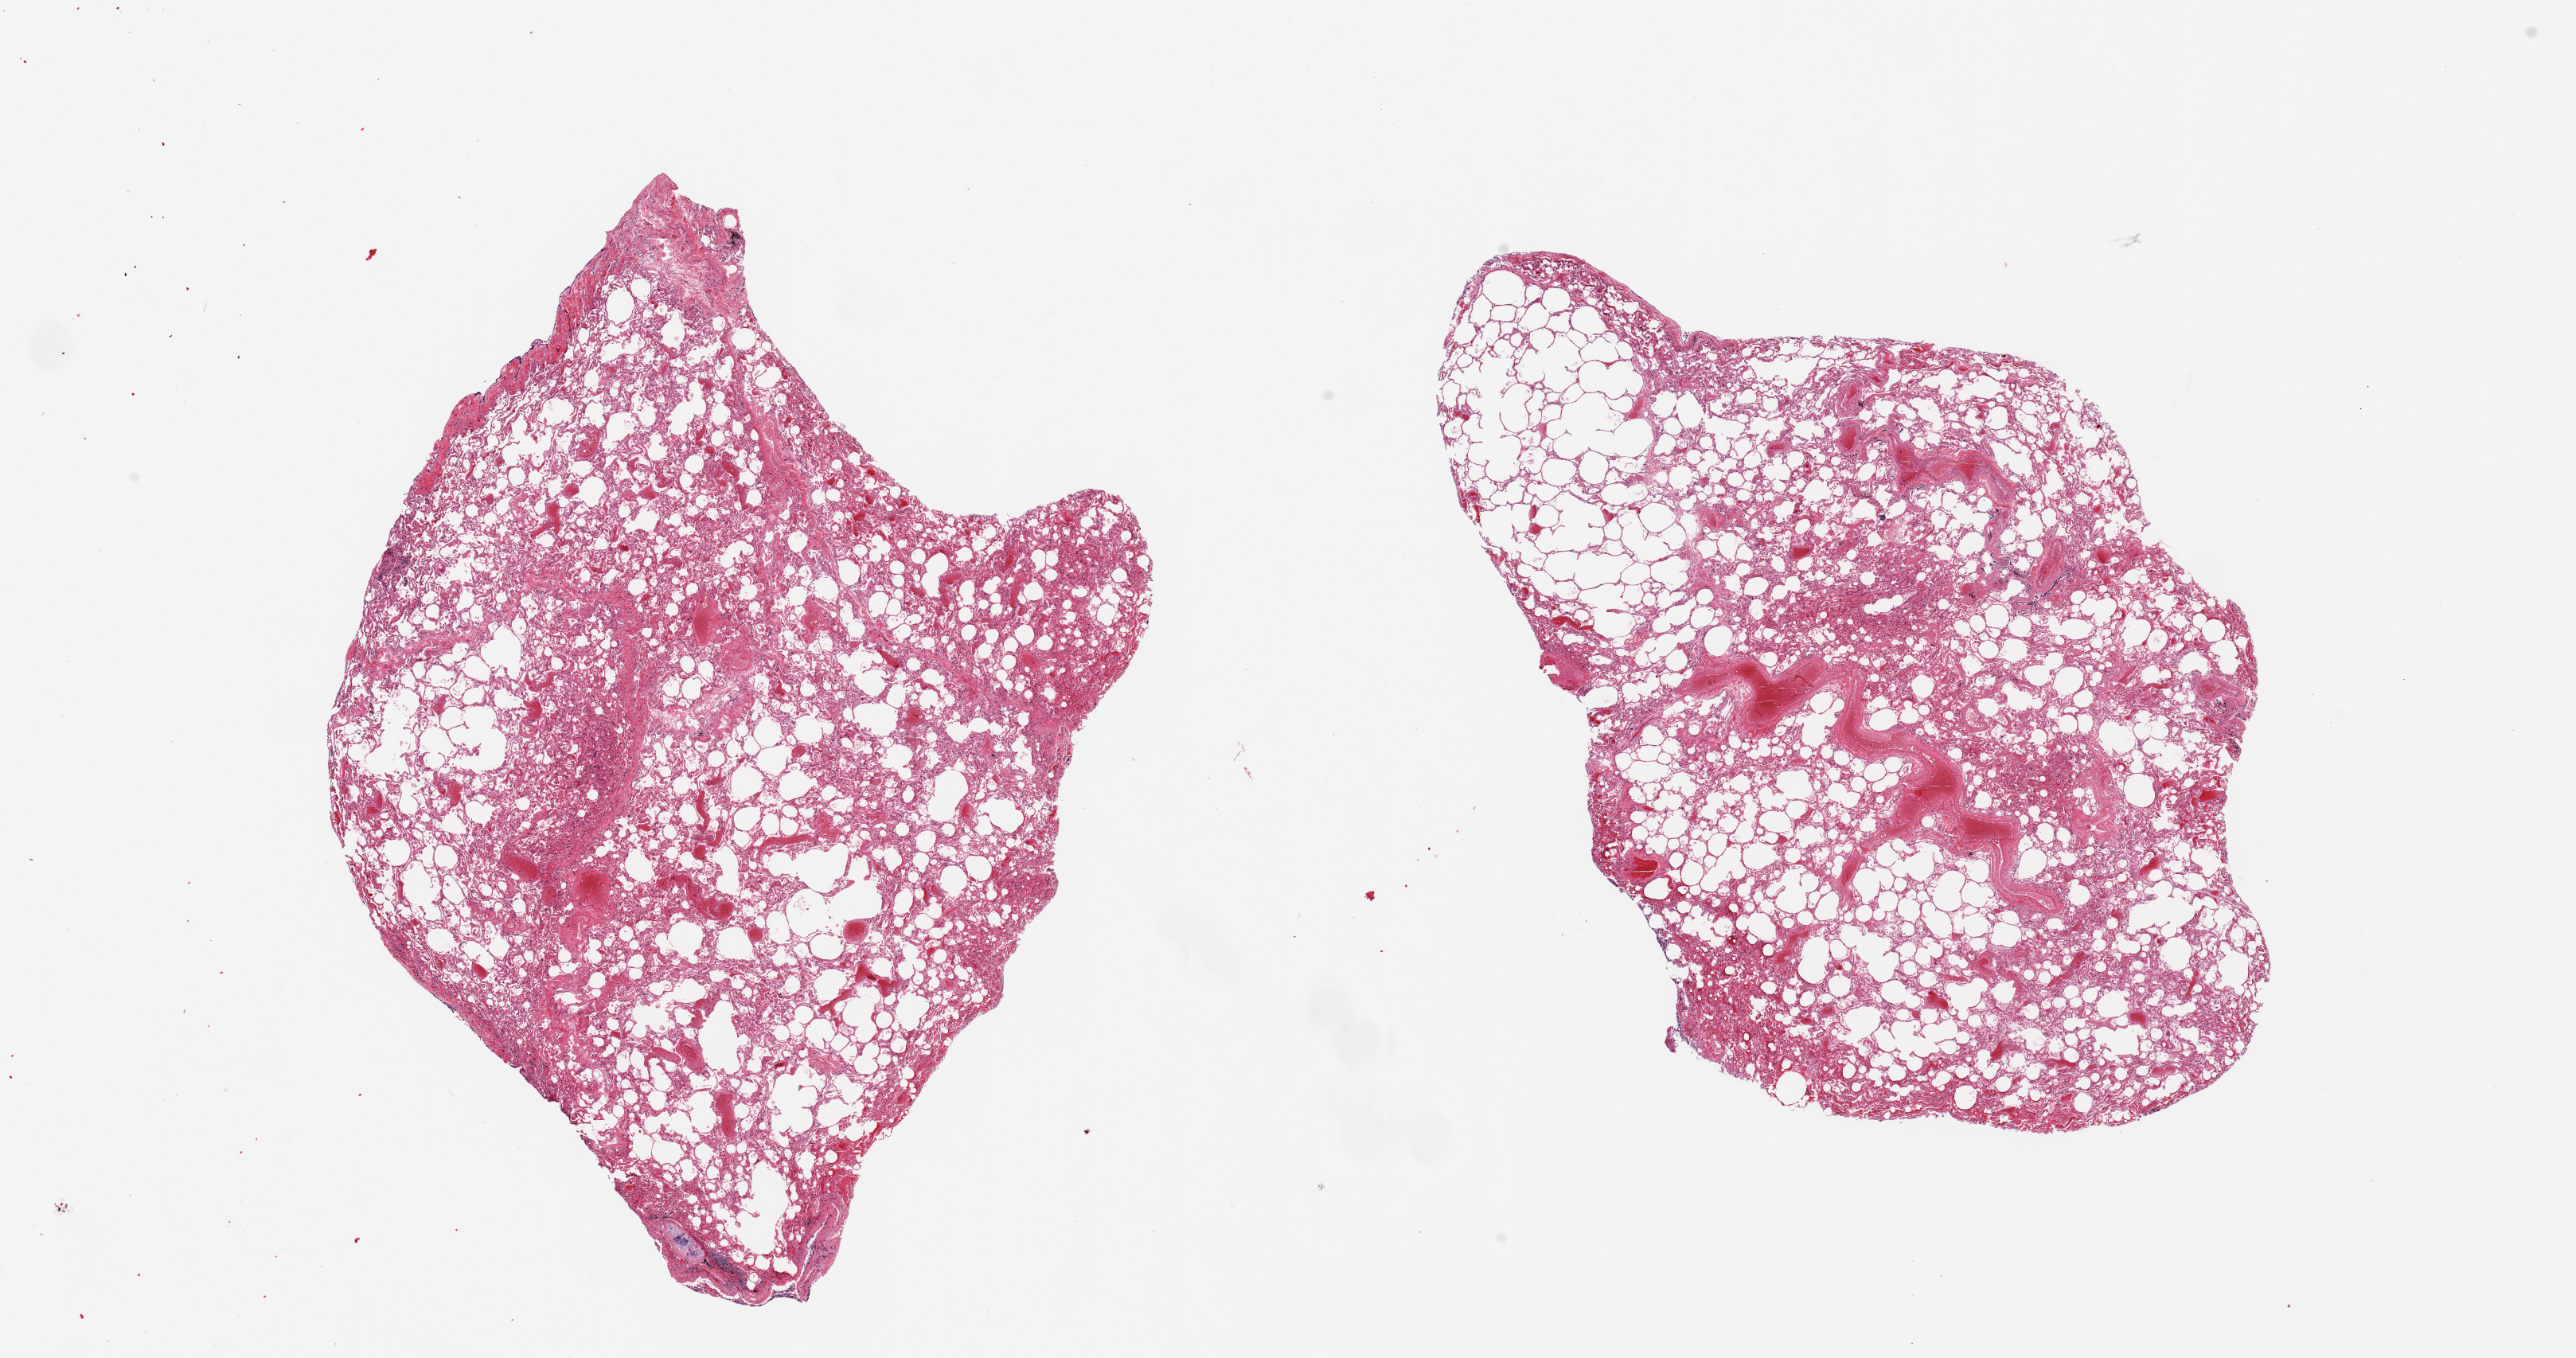
Hematoxylin and eosin (H&E) whole-slide image, brightfield, low-resolution overview of the scanned area, about 25.6 x 13.5 mm (slide scanned at 20x); PAXgene-fixed paraffin-embedded (PFPE) section; target tissue: lung; donor tissue sample.
* review note (as recorded): 2 pieces, 9x7 & 9x8mm; badly autolyzed